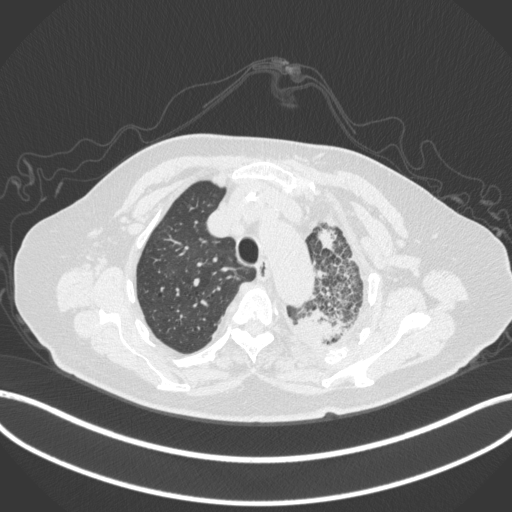
Chest CT, one axial slice; position 312 of 399 along the scan axis; reconstruction kernel B31f; 120 kVp; lung window (W 1500 / L -600 HU); 512 × 512 image matrix, field of view 400 × 400 mm. Patient: female, 75 years. Case-level facts recorded for this patient, not image findings: clinical TNM (as recorded): T3 N3 M1.
Annotated regions visible in this slice (rectangle marked by the reading radiologist):
- lung tumour (recorded histology: adenocarcinoma): box from (x=294, y=305) to (x=345, y=345) px